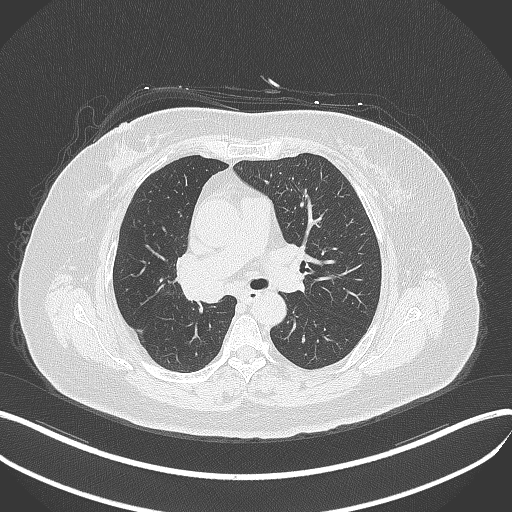
Chest CT, one axial slice. Position 215 of 376 along the scan axis. 120 kVp. Lung window (W 1500 / L -600 HU). 1 mm slice thickness. 512 × 512 image matrix, field of view 400 × 400 mm. Patient: female, 60 years. From the clinical record (not read from this slice): clinical TNM (as recorded): T1c N0 M0; histopathological grade: G1-G2.
Outlined on this slice (bounding box drawn by a radiologist):
- lung tumour (recorded histology: squamous cell carcinoma): bounding box <180,274,230,305> (left, top, right, bottom; pixels)